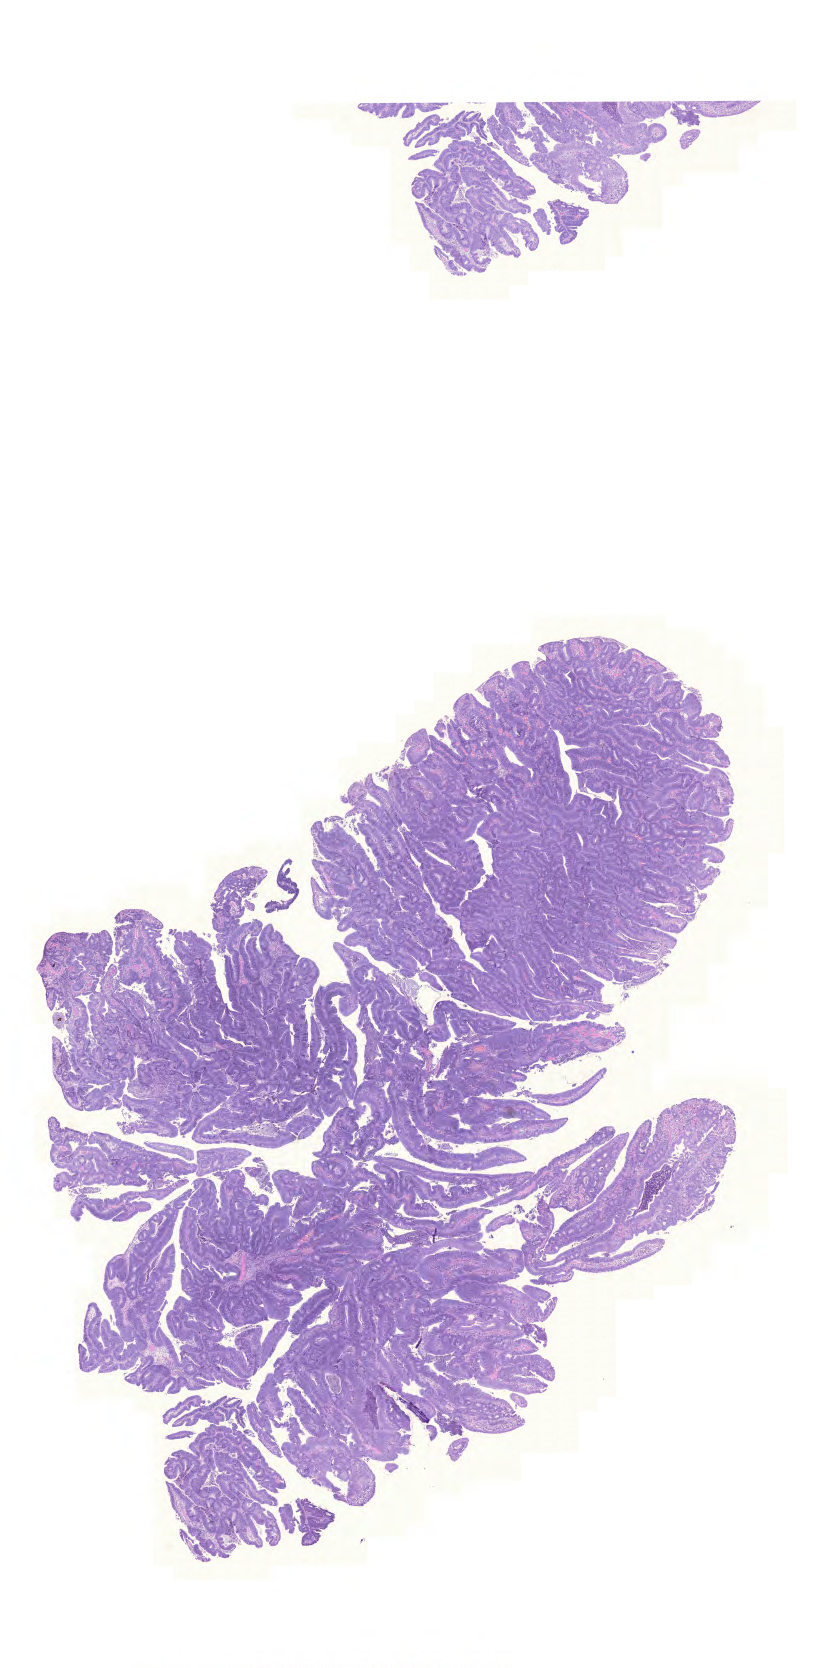
Hematoxylin and eosin (H&E) stained whole-slide image, shown as a low-resolution overview of the whole scanned area (about 12.2 x 24.8 mm, acquisition: 20x scan), formalin-fixed paraffin-embedded (FFPE) diagnostic section, sample: primary tumour, rectum. Patient: male, age at initial diagnosis 67 years.
Diagnosis: Adenocarcinoma, NOS (rectosigmoid junction).